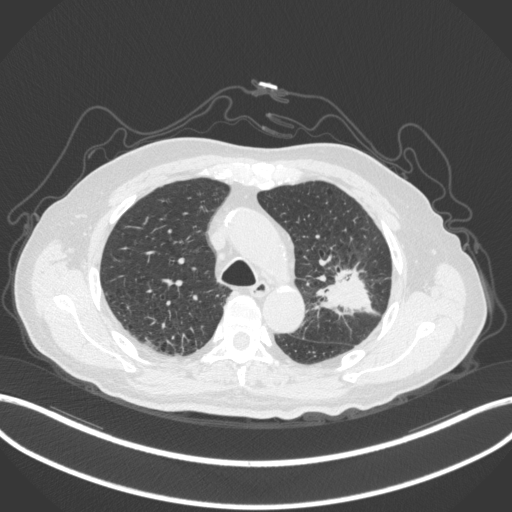
Chest CT, one axial slice; position 206 of 331 along the scan axis; reconstruction kernel B31f; 120 kVp; lung window (W 1500 / L -600 HU); 512 × 512 image matrix. Patient: male, 79 years. From the clinical record (not read from this slice): clinical TNM (as recorded): T2a N1 M1.
Structures marked on this image (rectangle marked by the reading radiologist):
- lung tumour (recorded histology: adenocarcinoma): bounding box <312,256,379,316> (left, top, right, bottom; pixels)